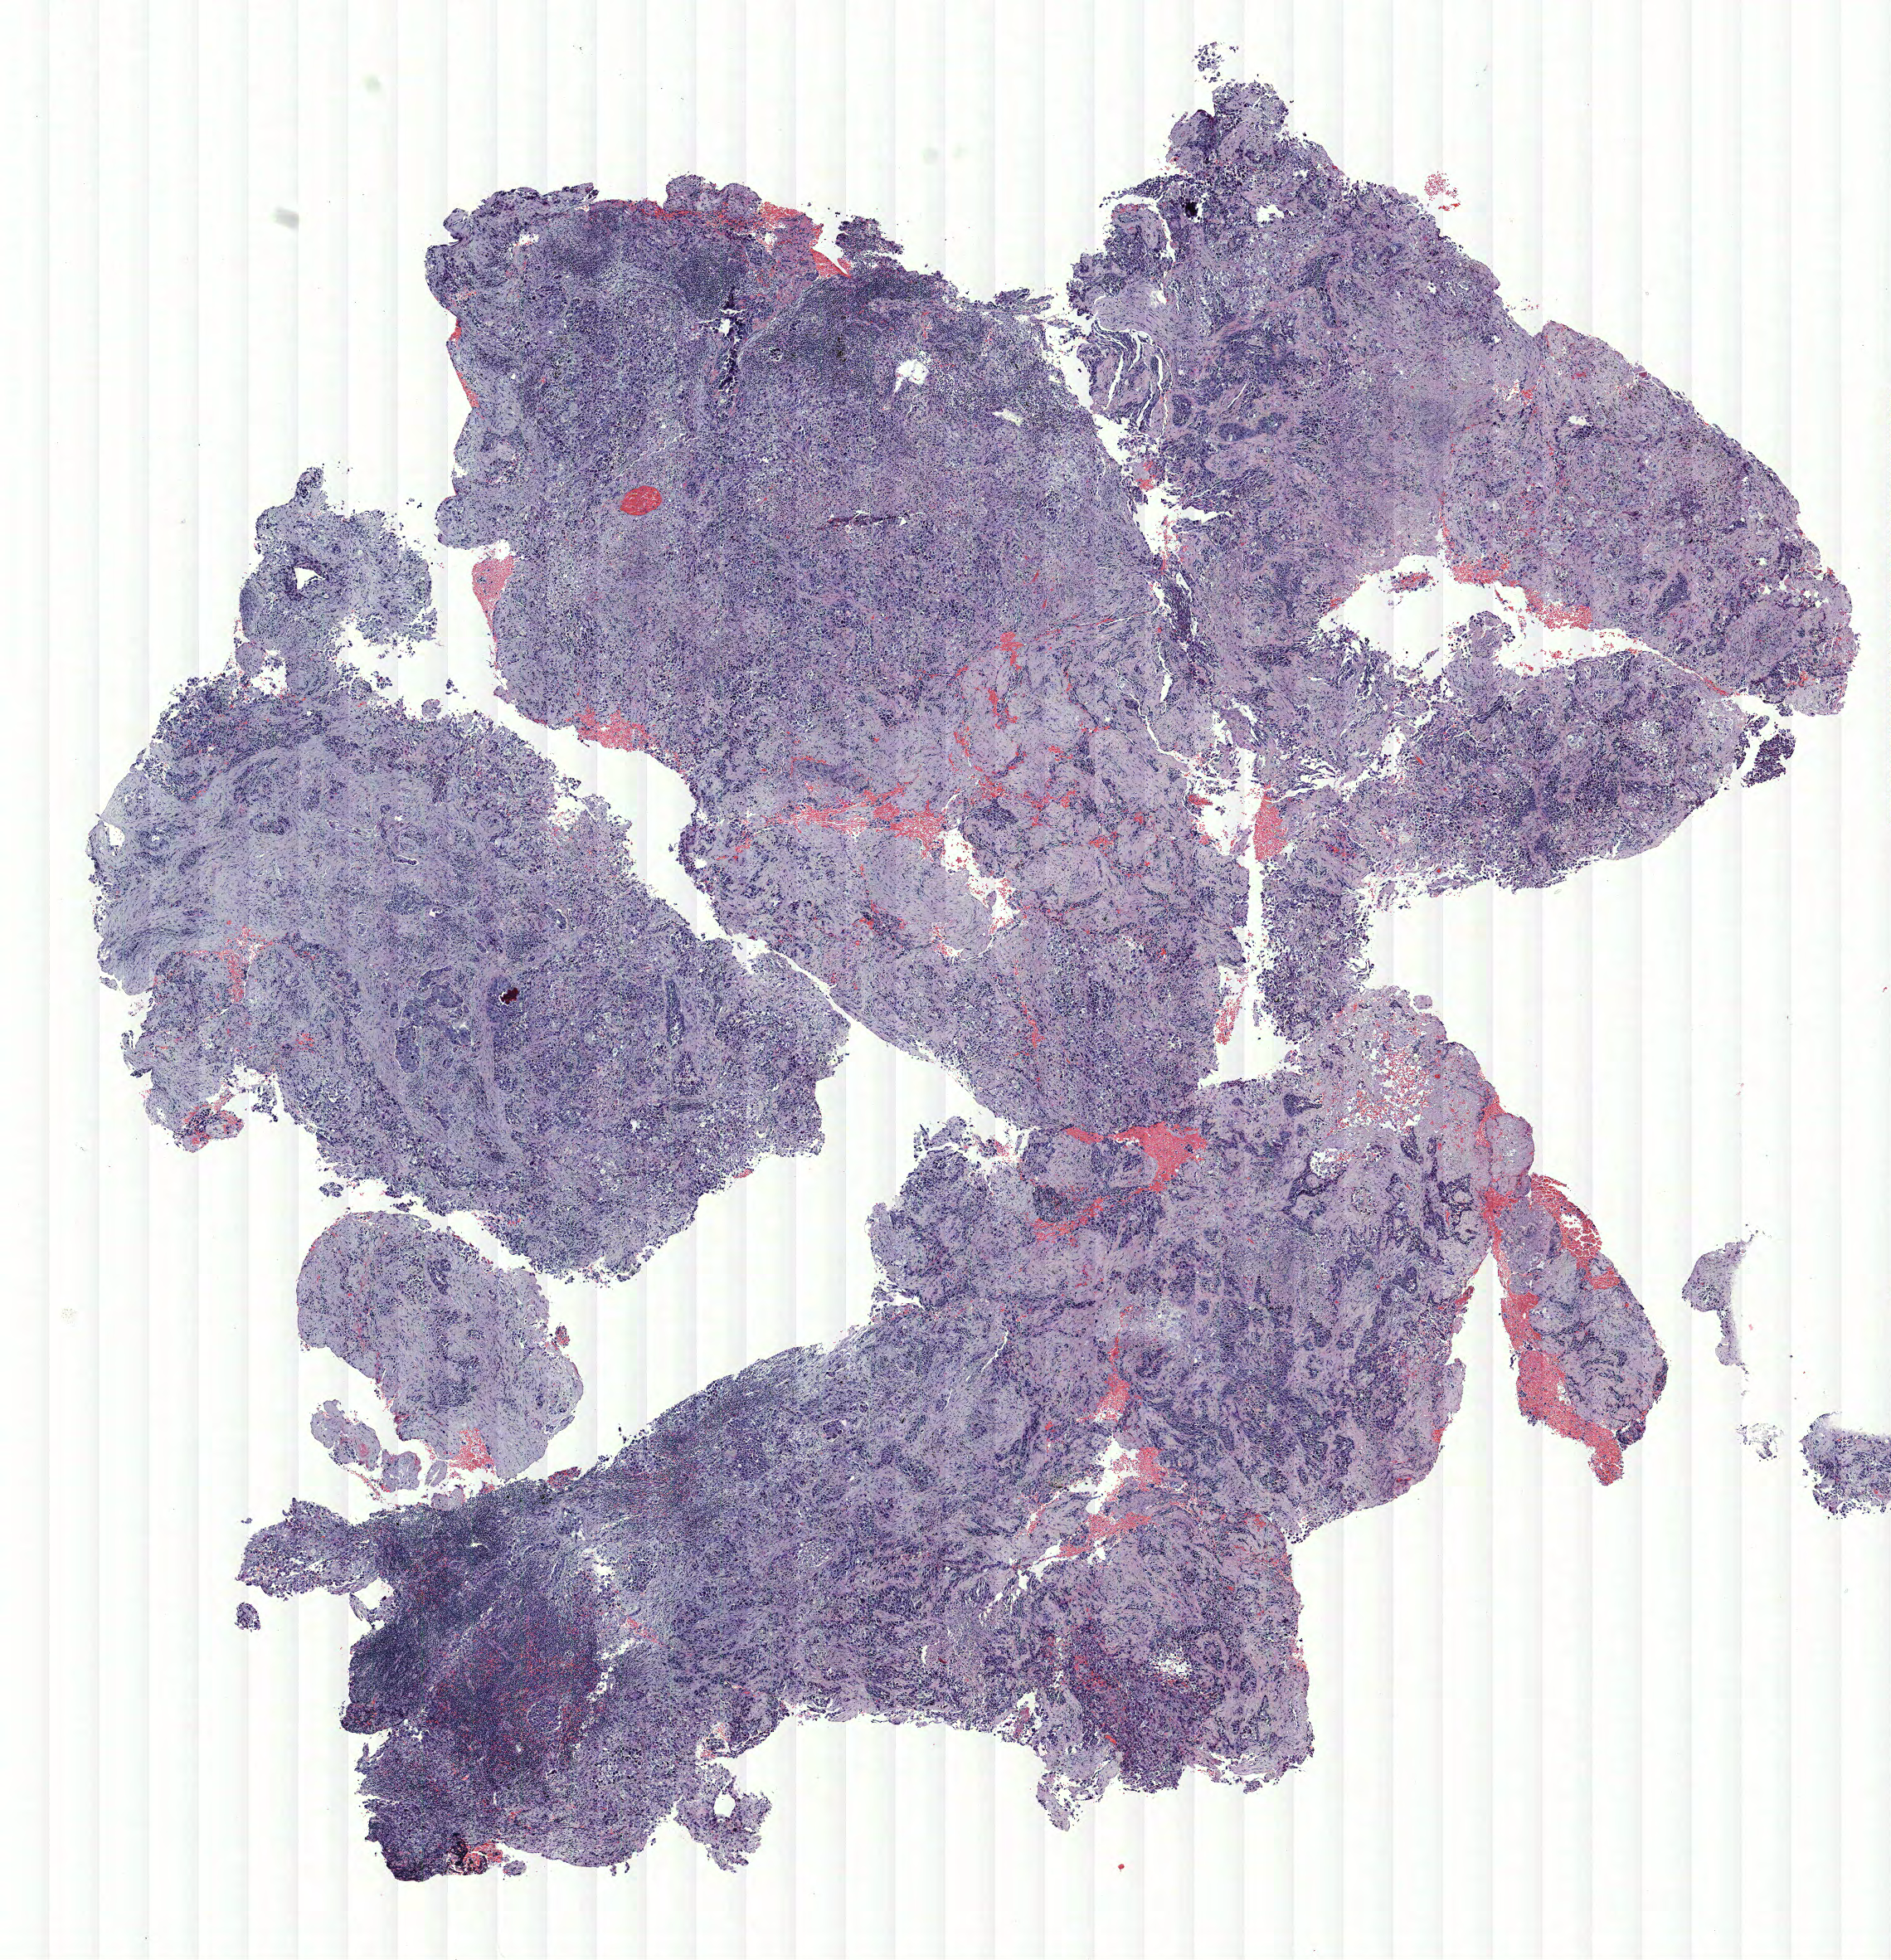
Whole-slide histology image, H&E, low-resolution overview of the scanned area, about 9.1 x 9.5 mm (acquisition: 40x scan); formalin-fixed paraffin-embedded (FFPE) section; lung. Male patient, aged 59 at enrolment. Current smoker at enrolment. Grade: cannot be assessed (GX).
Participant's lung-cancer diagnosis: Squamous cell carcinoma, NOS. Primary tumour location (clinical record): right upper lobe. Stage (AJCC 6th edition): IIIA. Tumour size (pathology): 7 mm.